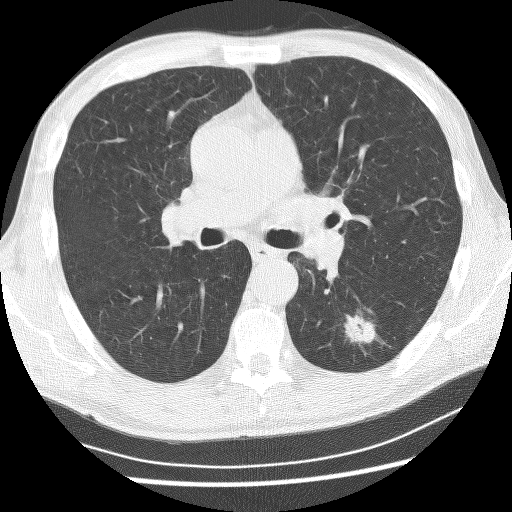
Low-dose screening chest CT, one axial slice; slice 148 of 253 in the series (ordered by position); 120 kVp; lung window (W 1500 / L -600 HU); 2.5 mm slice thickness; 512 × 512 image matrix, field of view 340 × 340 mm.
Annotated regions visible in this slice (manually delineated by an expert):
- lesion 1 (tumor, lower lobe of left lung): bounding box <344,314,376,344> (left, top, right, bottom; pixels)